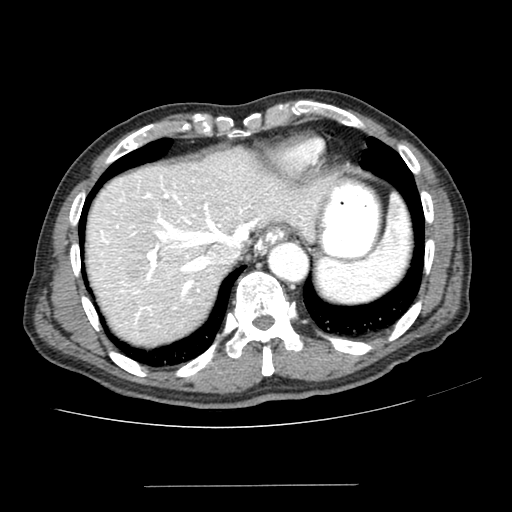
Contrast-enhanced abdominal CT (liver protocol), one axial slice; slice 171 of 187 in the series (ordered by position); reconstruction kernel SOFT; 100 kVp; one of 2 acquisitions stored at this slice position; soft-tissue window (W 400 / L 40 HU); 2.5 mm slice thickness; 512 × 512 image matrix. Case-level facts recorded for this patient, not image findings: diagnosis: hepatocellular carcinoma (patient treated with transarterial chemoembolisation; whether this scan precedes or follows treatment is not stated here); TNM stage (as recorded): Stage-I; Child-Pugh class: A; tumour differentiation: poorly differentiated; tumour nodularity: uninodular.
Annotated regions visible in this slice (semi-automatic segmentation, software-assisted and operator-edited):
- liver parenchyma outside the tumour (the mass and vessels are separate outlines, so this box may not span the whole liver): bounding box [x1, y1, x2, y2] px = [86, 148, 320, 346]
- mass: [120, 251, 150, 283]
- liver vessels: [101, 176, 304, 324]